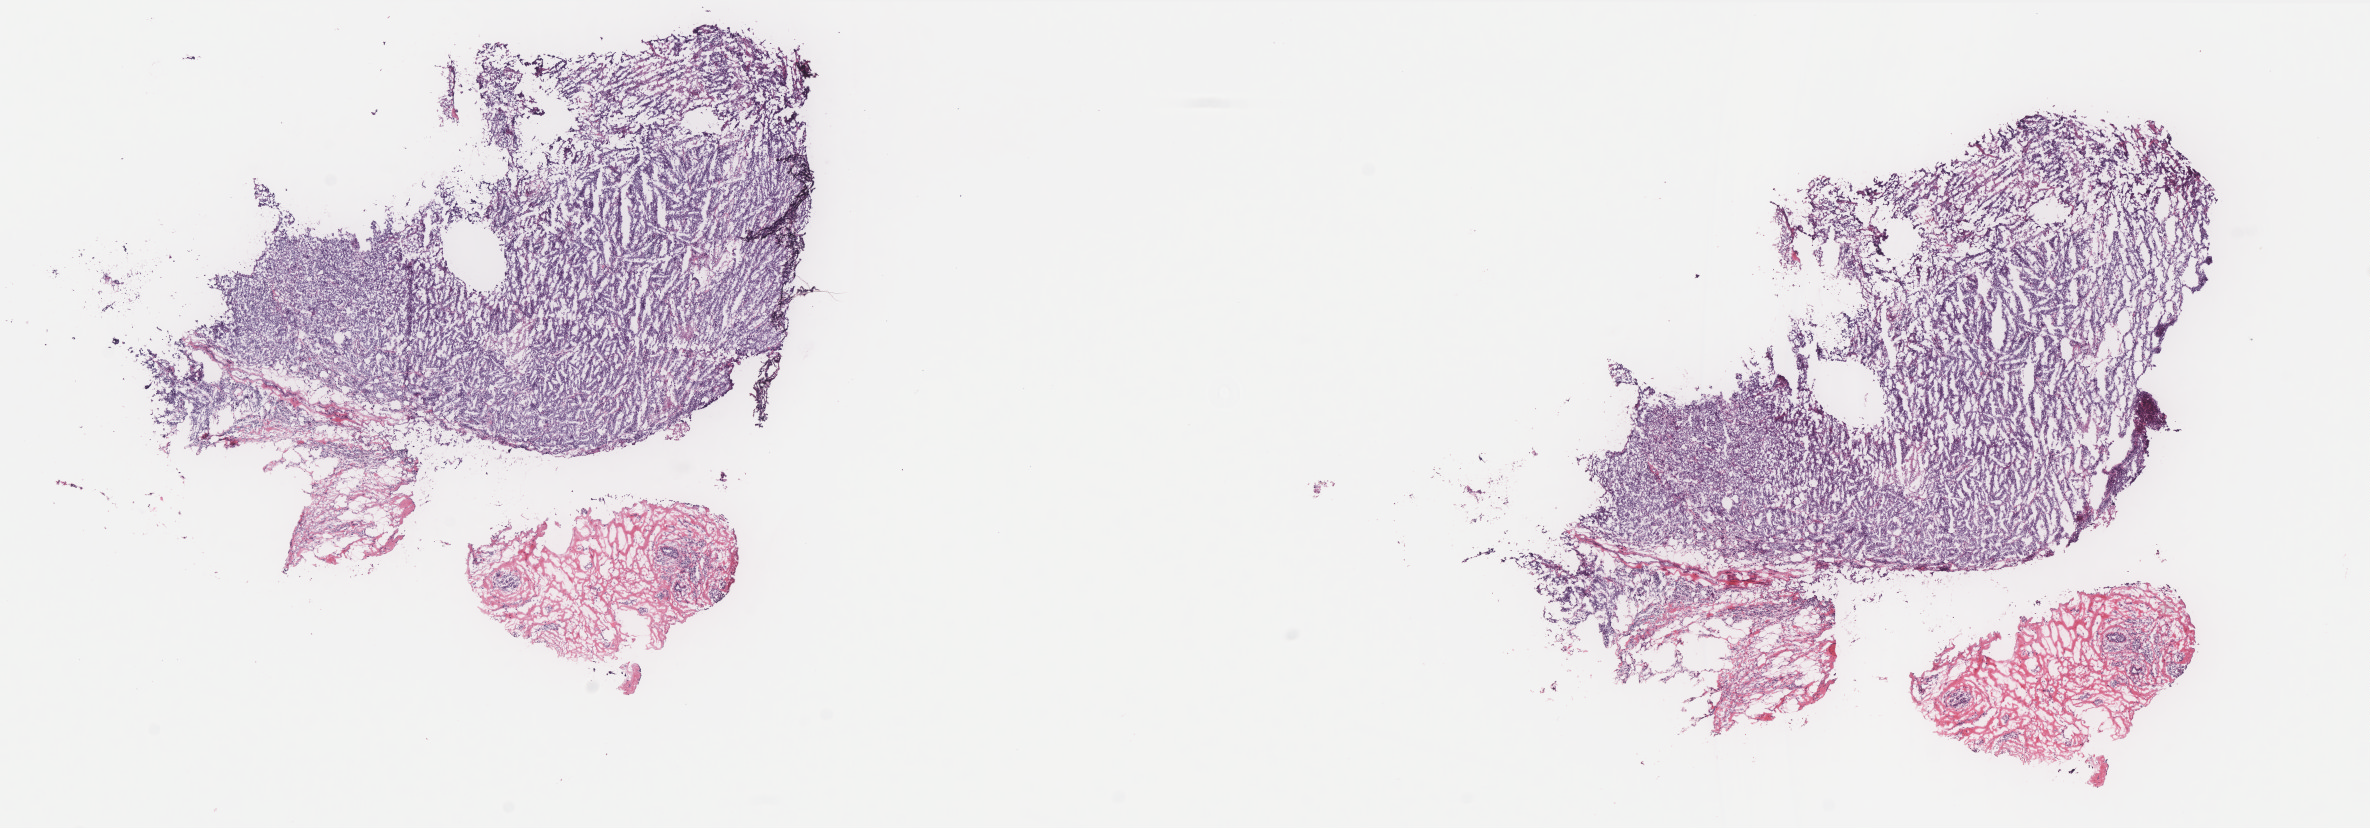
Whole-slide histology image, H&E — whole scanned area (about 19.0 x 6.6 mm, acquisition: 40x scan) shown as a low-resolution overview, frozen section from the top of the tissue portion, primary tumour sample from the breast. Female, age 35 years at initial diagnosis. Pathologist review of this section (percent, as recorded): tumour cells 75%, tumour nuclei 90%.
Histologic diagnosis: Infiltrating duct carcinoma, NOS.